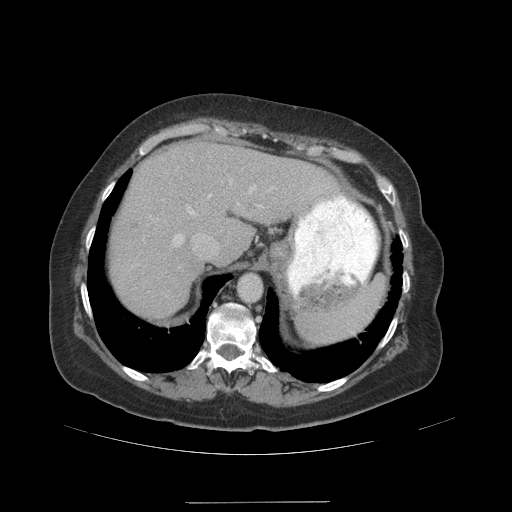
Contrast-enhanced abdominal CT (liver protocol), one axial slice; position 77 of 99 along the scan axis; reconstruction kernel STANDARD; soft-tissue window (W 400 / L 40 HU); 512 × 512 image matrix. Case-level facts recorded for this patient, not image findings: diagnosis: hepatocellular carcinoma (patient treated with transarterial chemoembolisation; whether this scan precedes or follows treatment is not stated here); TNM stage (as recorded): Stage-IVA; Child-Pugh class: A; tumour nodularity: multinodular.
Annotated regions visible in this slice (semi-automatically segmented with operator editing):
- abdominal aorta: bounding box (x1, y1, x2, y2) in pixels: (238, 273, 262, 302)
- liver parenchyma outside the tumour (the mass and vessels are separate outlines, so this box may not span the whole liver): (110, 142, 336, 318)
- liver vessels: (173, 181, 273, 247)